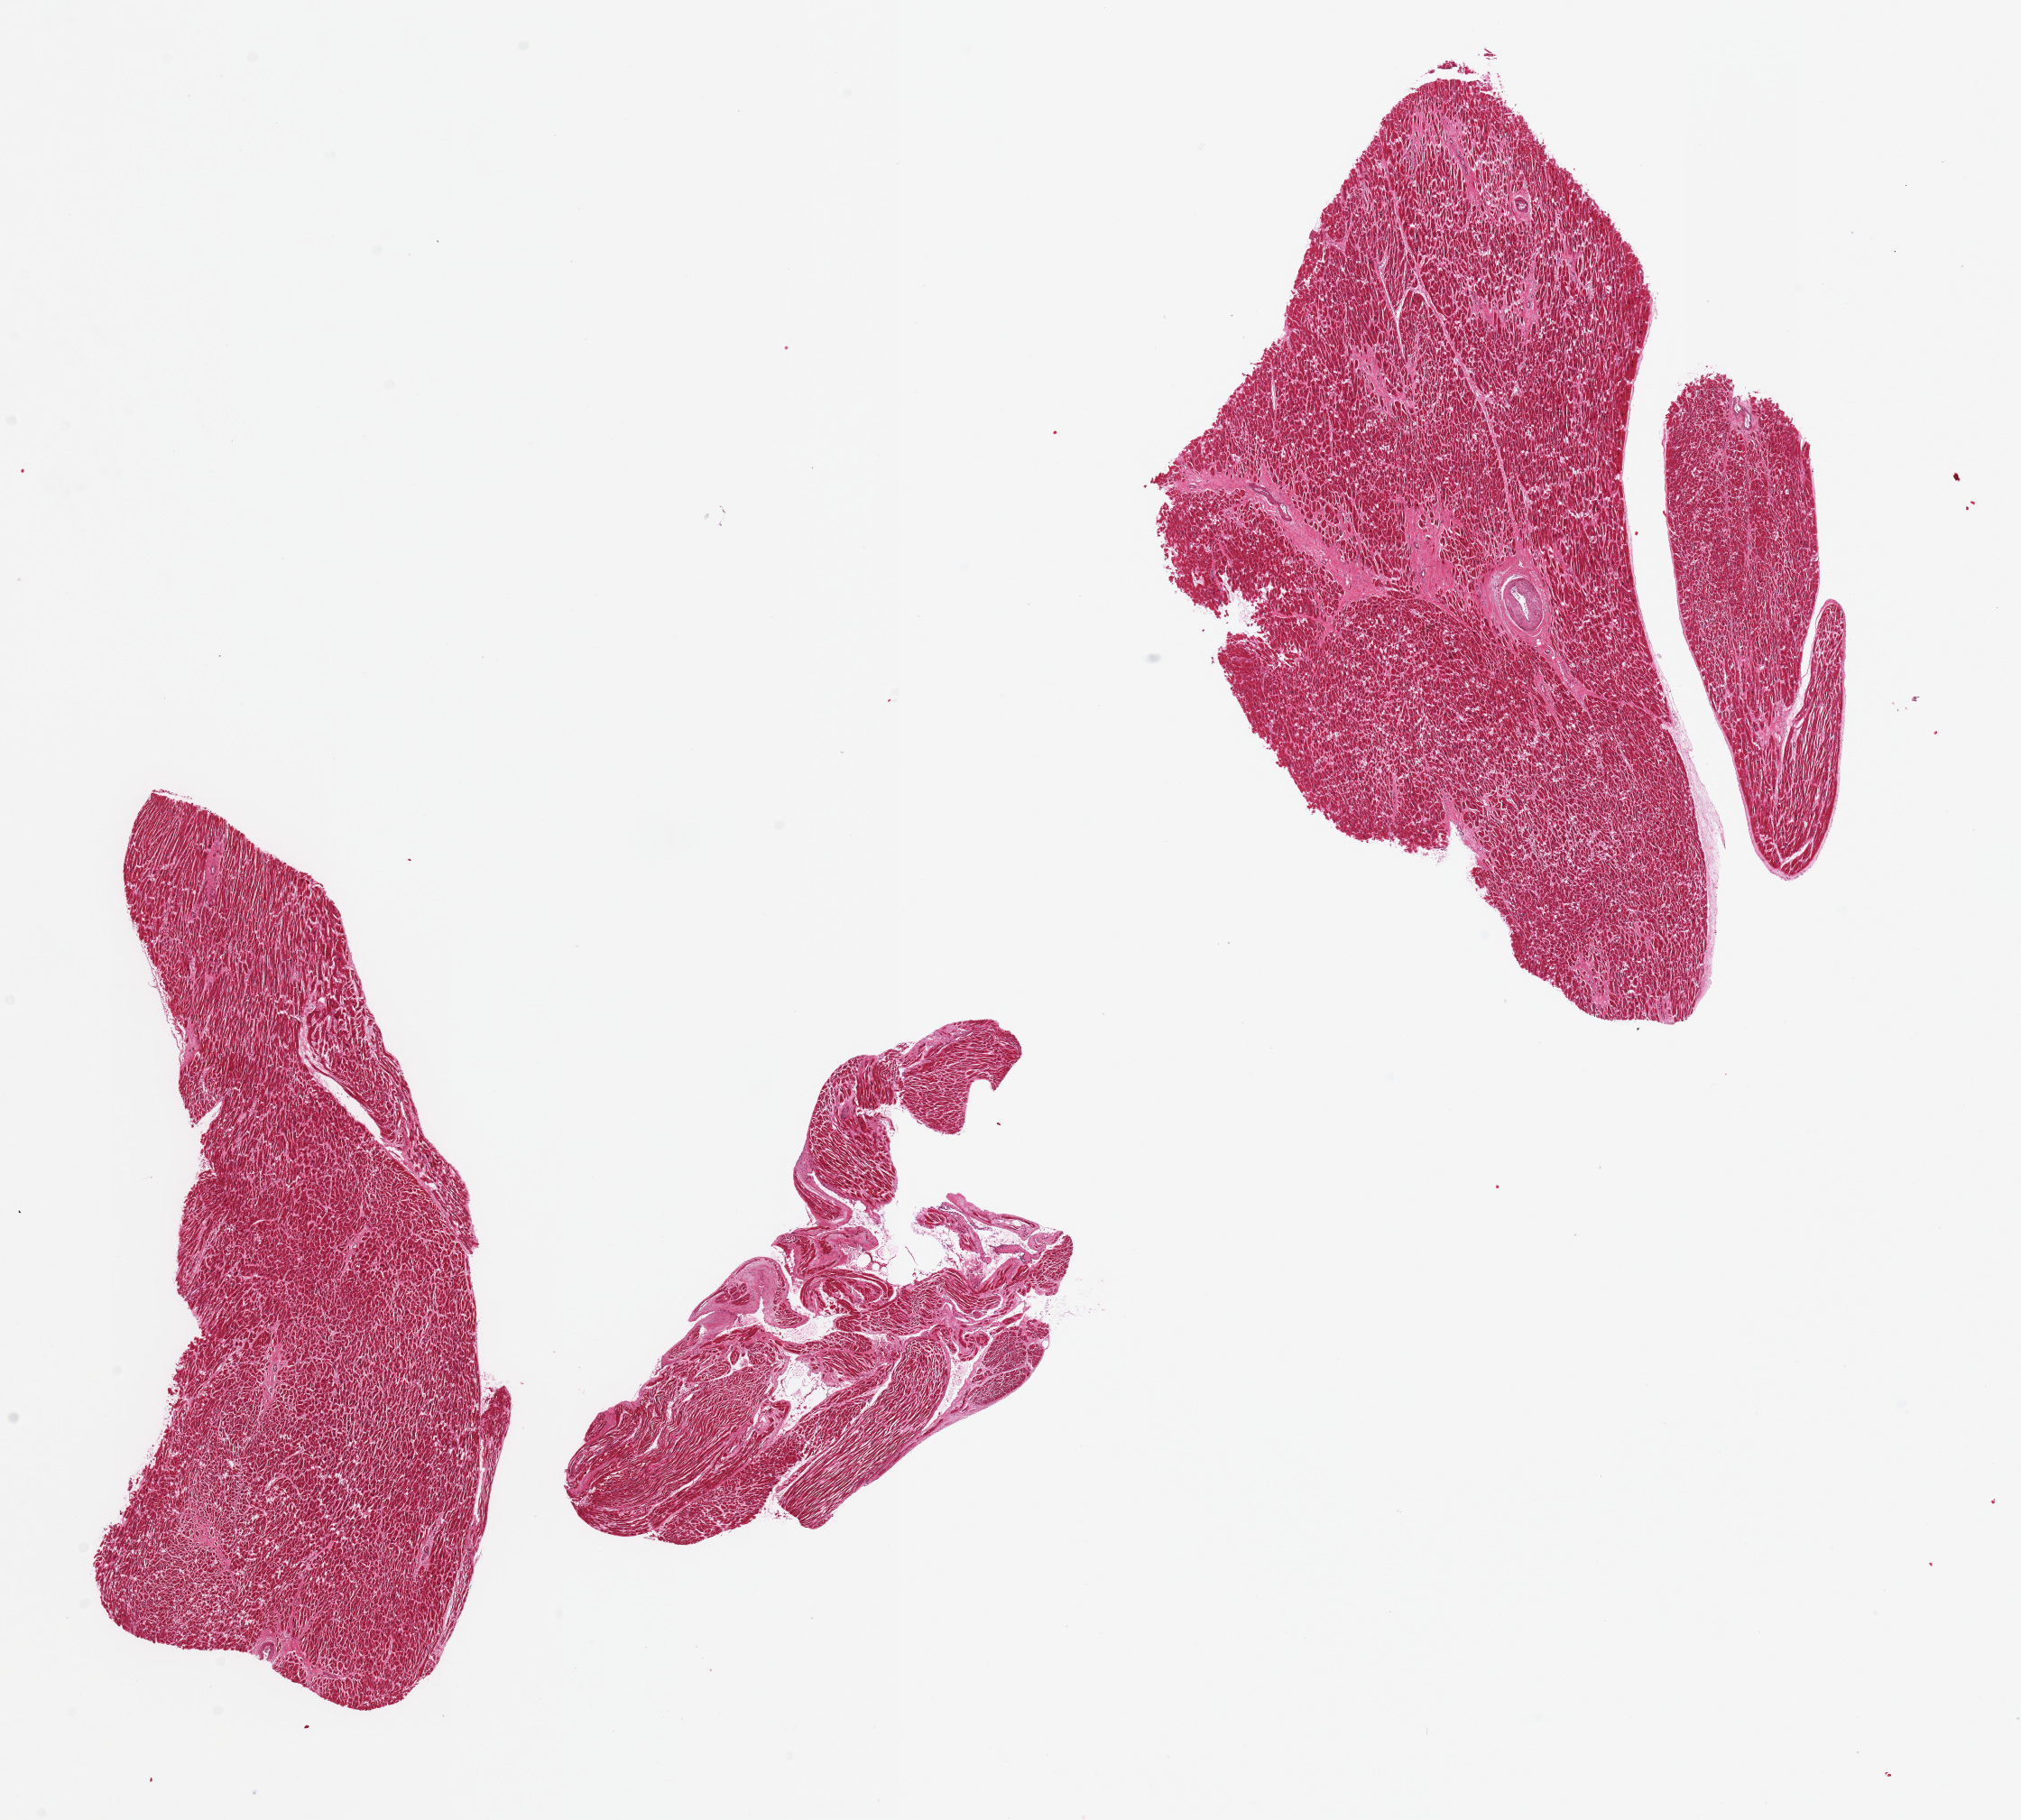
H&E whole-slide image — low-resolution overview of the scanned area, about 17.7 x 16.0 mm, PAXgene-fixed, paraffin-embedded tissue, section of heart (target tissue), tissue donor sample. Donor: female.
* reviewer comment on this tissue sample: 3 pieces; scattered focal interstitial fibrosis; myofibers are hypertrophied